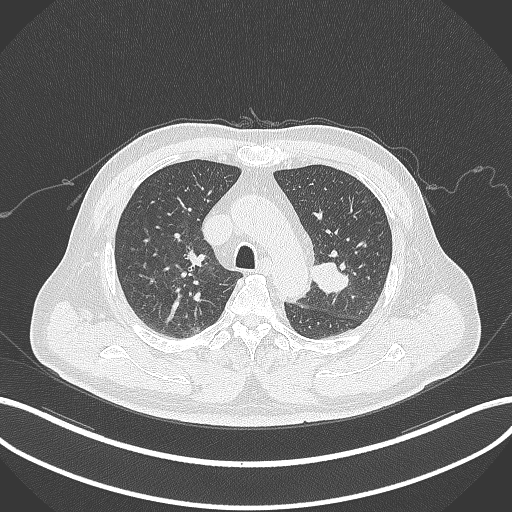
Chest CT, one axial slice. Position 218 of 286 along the scan axis. 120 kVp. Lung window (W 1500 / L -600 HU). 1 mm slice thickness. 512 × 512 image matrix, field of view 400 × 400 mm. Male patient, age 67 years. Case-level facts recorded for this patient, not image findings: clinical TNM (as recorded): T2a N1 M0; histopathological grade: G3.
Structures marked on this image (bounding box drawn by a radiologist):
- lung tumour (recorded histology: adenocarcinoma): bounding box <307,259,352,295> (left, top, right, bottom; pixels)